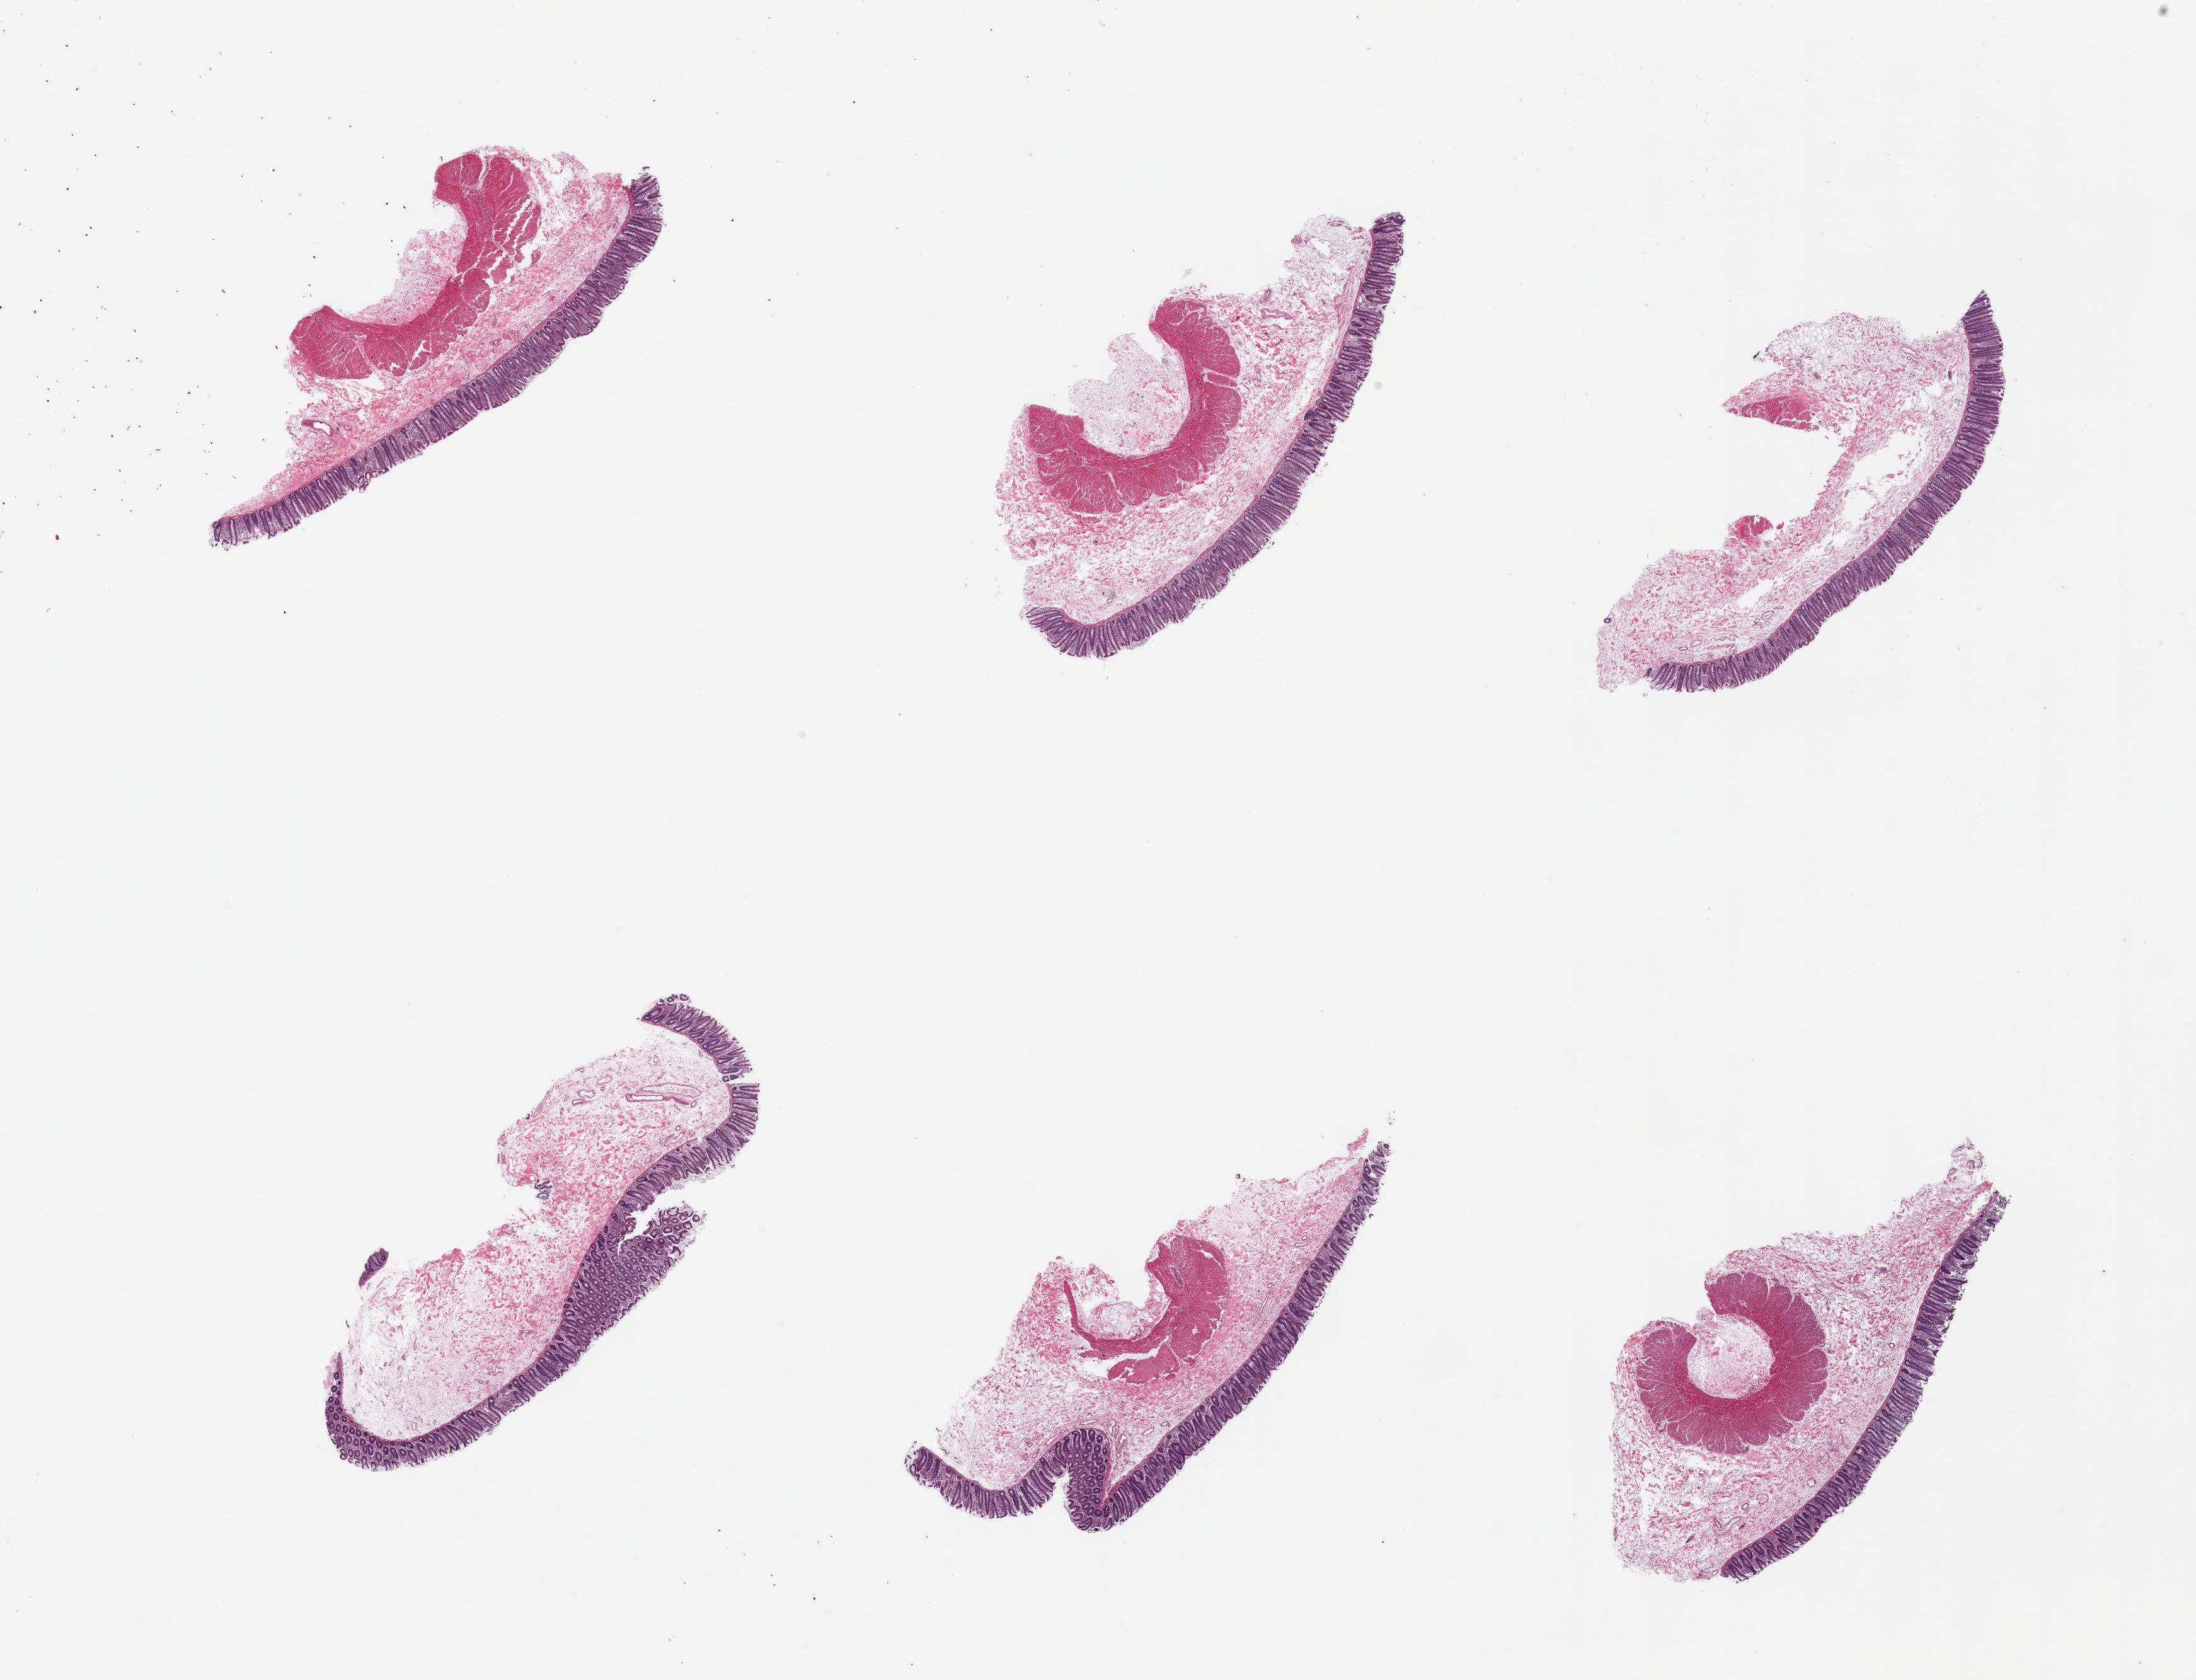
Whole-slide image, hematoxylin and eosin (H&E) stain — low-resolution overview of the scanned area, about 27.6 x 21.1 mm. PAXgene-fixed paraffin-embedded (PFPE) section. Target tissue: transverse colon. Tissue donor sample. Male donor.
Review note (as recorded): 6 pieces, well preserved; mucosa is ~15-20% thickness.